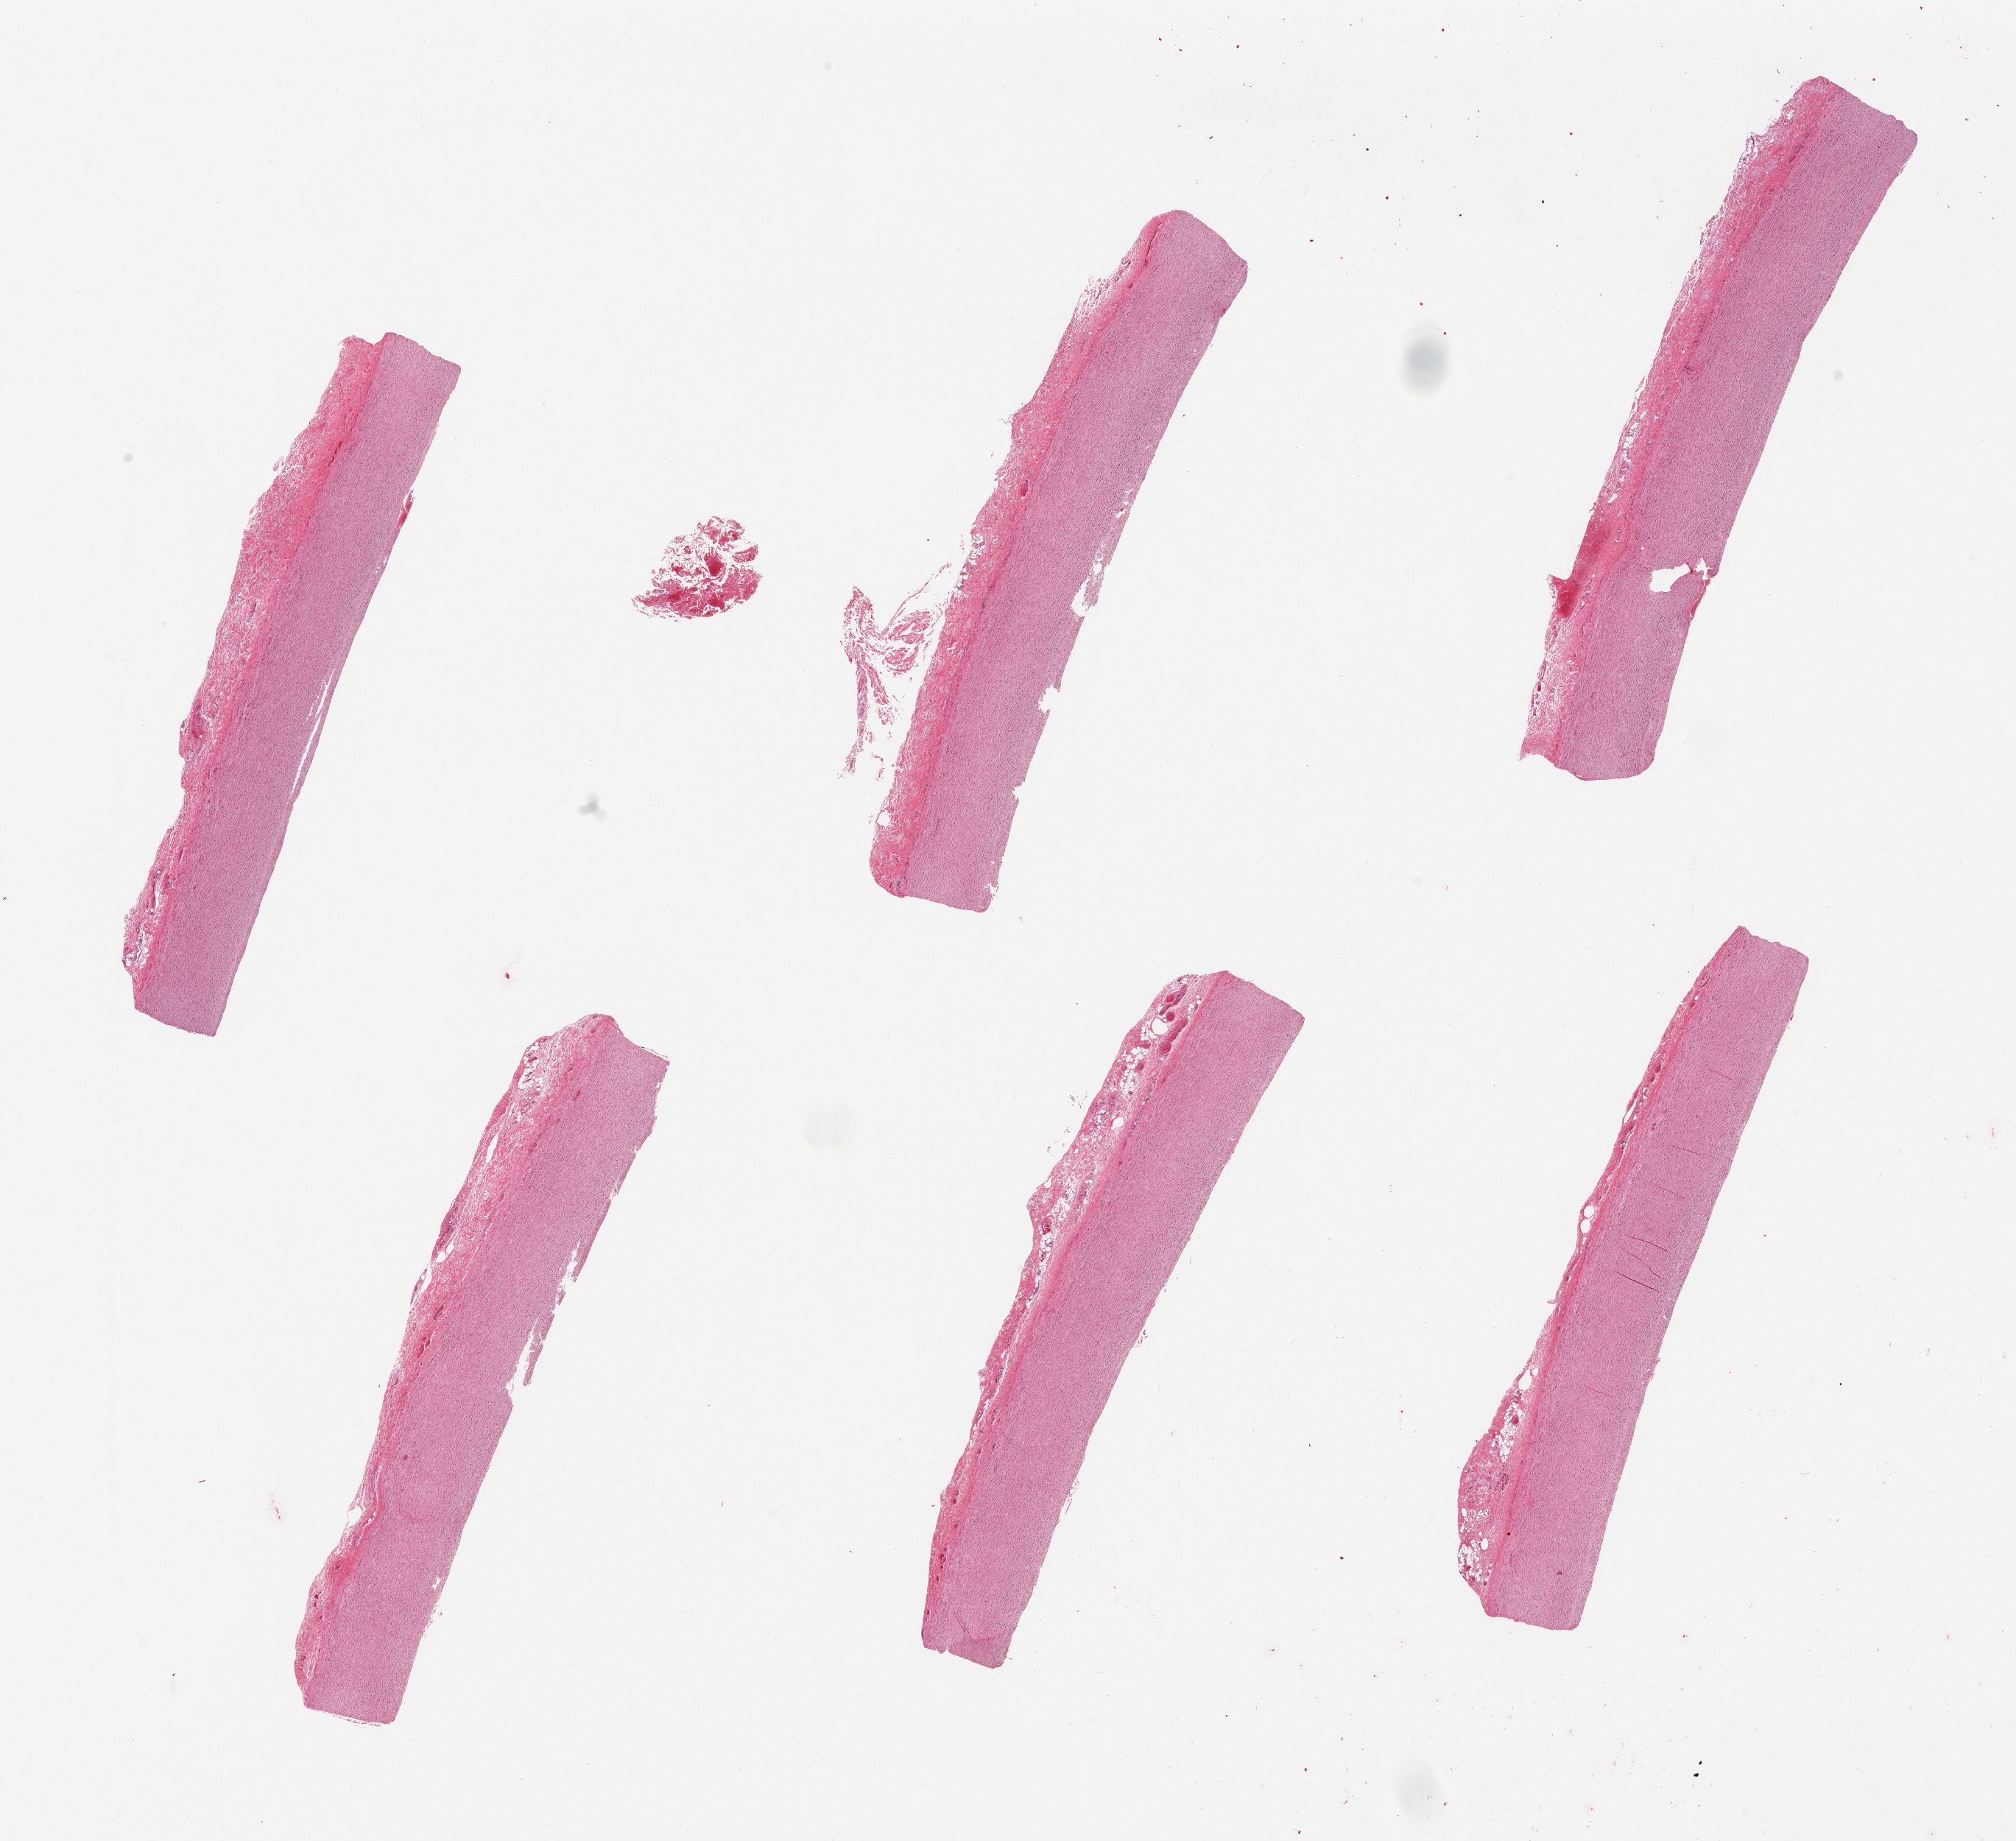
Digitized hematoxylin and eosin (H&E)-stained section, whole scanned area (about 21.7 x 19.8 mm) shown as a low-resolution overview. PAXgene-fixed paraffin-embedded (PFPE) section. Target tissue: aorta. Tissue donor sample. Donor sex: female.
• reviewer comment on this tissue sample: 6 pieces. Adherent serosa/vasa vasorum ~0.5mm thick on all